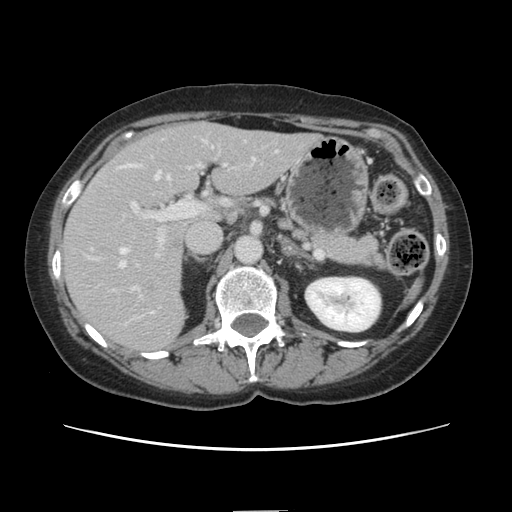
Contrast-enhanced abdominal CT, one axial slice. Slice 77 of 141 in the series (ordered by position). 120 kVp. Soft-tissue window (W 400 / L 40 HU). 2.5 mm slice thickness. 512 × 512 image matrix, field of view 350 × 350 mm. Female patient, age 63 years. From the clinical record (not read from this slice): diagnosis: colorectal cancer liver metastases, imaged before liver resection; multiple liver metastases: yes; largest metastasis: 3.2 cm.
Structures marked on this image (expert manual segmentation):
- hepatic veins: bounding box (x1, y1, x2, y2) in pixels: (87, 158, 255, 269)
- liver: (64, 124, 314, 353)
- planned liver remnant (the part of the liver to remain after resection): (175, 124, 315, 196)
- portal vein (with intrahepatic branches): (127, 164, 201, 313)